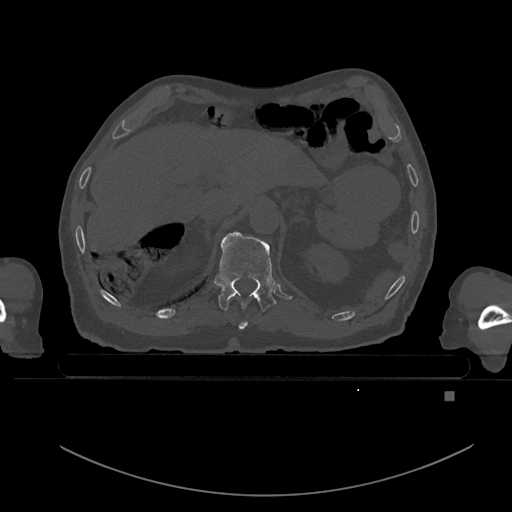
CT including the spine, one axial slice; slice 40 of 969 in the series (ordered by position); bone window (W 1800 / L 400 HU); 0.5 mm slice thickness; 512 × 512 image matrix, field of view 456 × 456 mm. Male patient, age 82 years. Case-level facts recorded for this patient, not image findings: primary cancer: prostate.
Annotated regions visible in this slice (semi-automatic segmentation, software-assisted and operator-edited):
- T10 vertebra: bounding box [x1, y1, x2, y2] px = [239, 321, 248, 329]
- T11 vertebra: [214, 231, 276, 312]